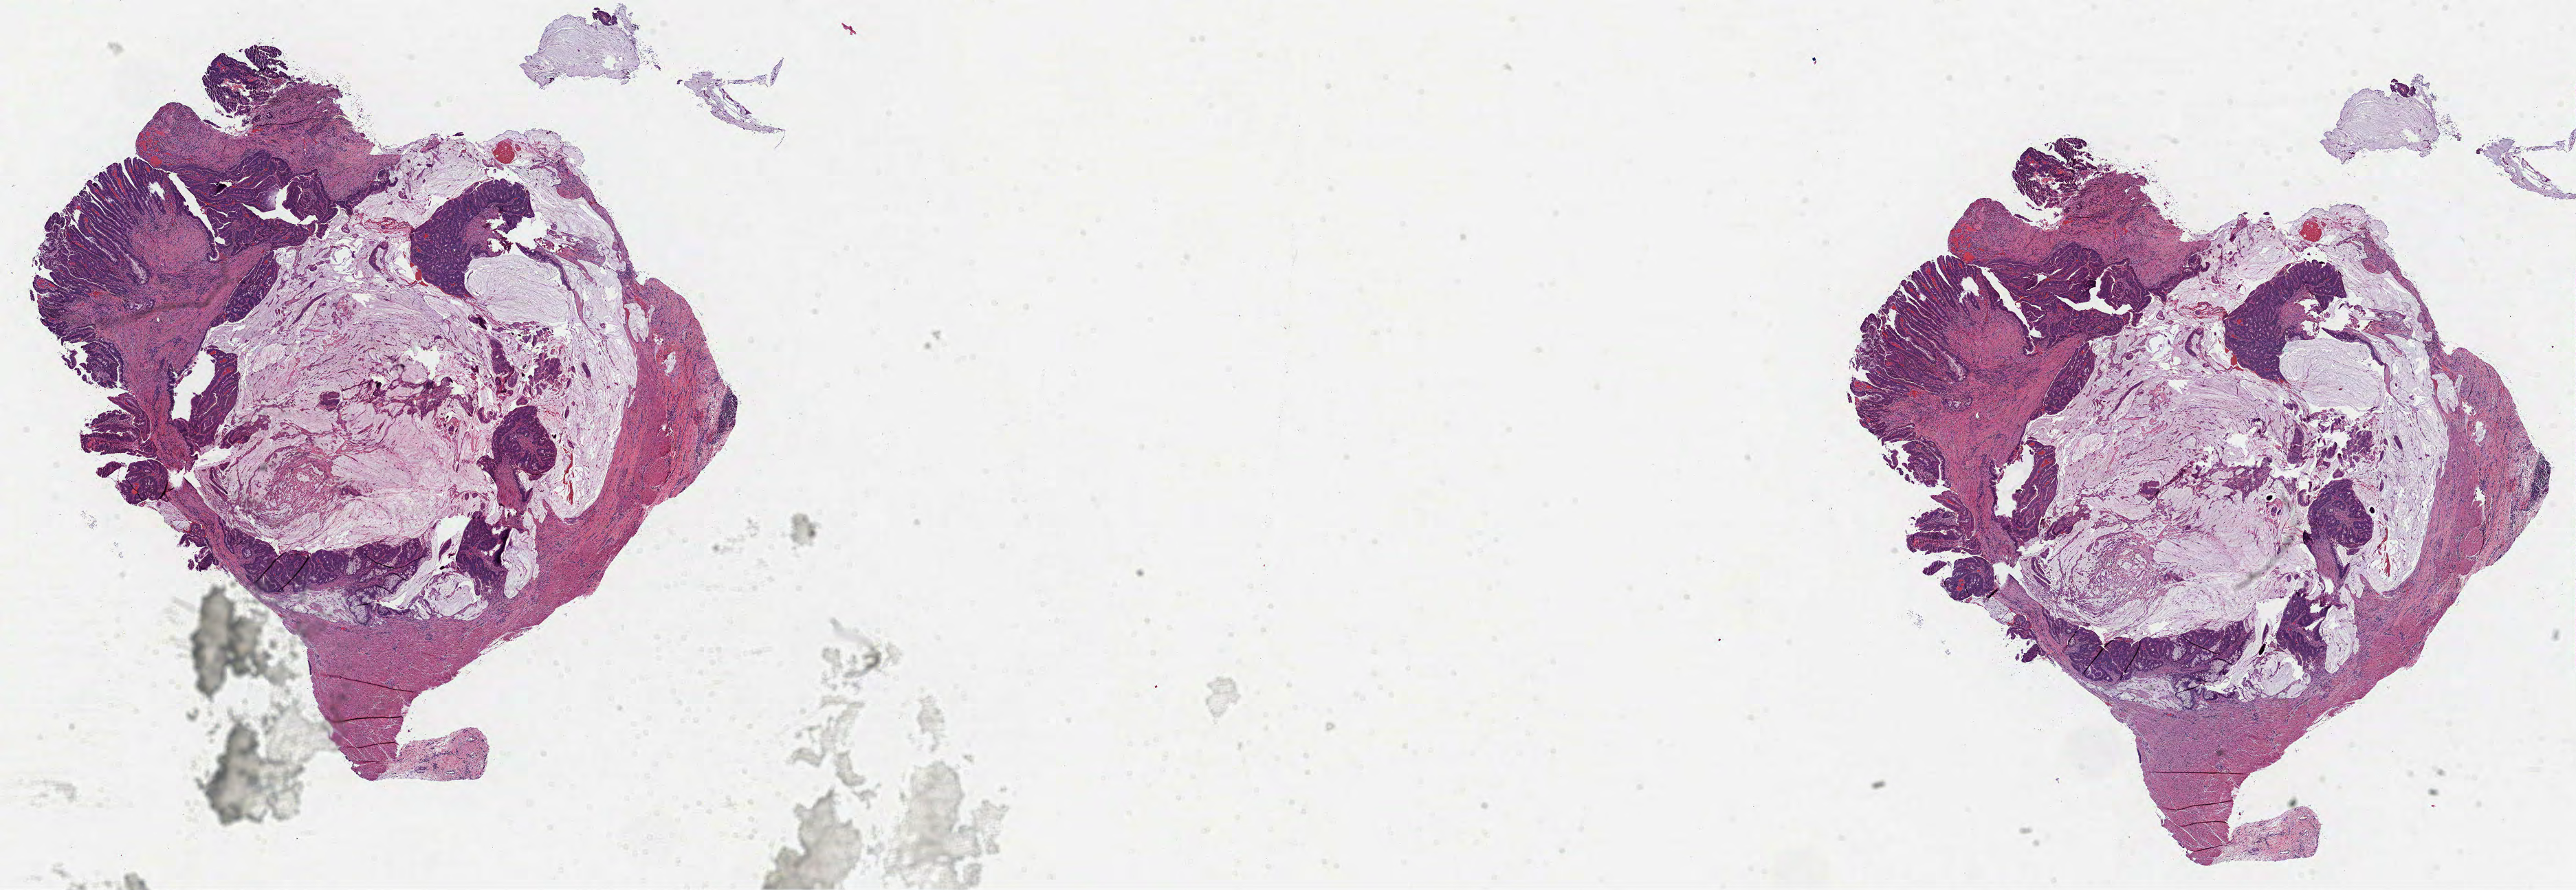
H&E-stained whole-slide image — low-resolution overview of the scanned area, about 30.2 x 10.4 mm (slide scanned at 40x); formalin-fixed paraffin-embedded (FFPE) diagnostic section; primary tumour sample from the colon. Male, age 73 years at initial diagnosis.
Histologic diagnosis: Adenocarcinoma, NOS. AJCC pathologic stage: IIA.